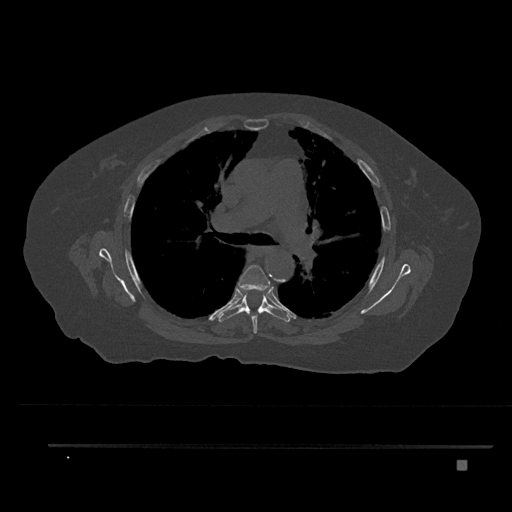
CT including the spine, one axial slice. Slice 545 of 797 in the series (ordered by position). 120 kVp. Bone window (W 1800 / L 400 HU). 512 × 512 image matrix. Patient: female, 76 years. From the clinical record (not read from this slice): primary cancer: lung; vertebrae with lytic lesions (as recorded): T11, L3.
Structures marked on this image (semi-automatic segmentation, software-assisted and operator-edited):
- T5 vertebra: bounding box [x1, y1, x2, y2] px = [238, 265, 271, 333]
- T6 vertebra: [219, 291, 290, 322]